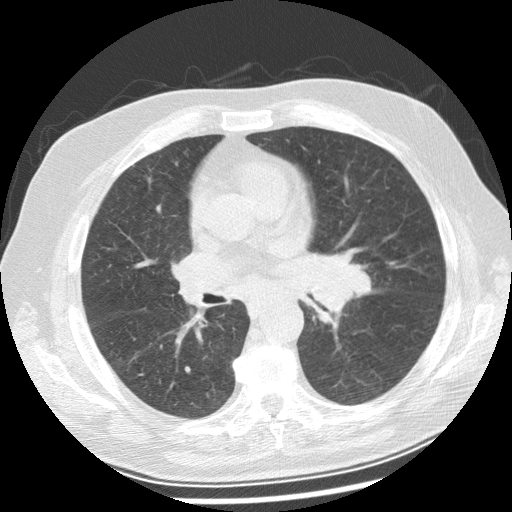
Axial slice from a low-dose chest CT screening exam; baseline screening round; lung window (W 1500 / L -600 HU); standard (soft-tissue) reconstruction kernel (STANDARD); 120 kVp; 512 × 512 image matrix. Male participant, aged 70 years at enrolment.
- Expert-annotated lung lesion, bounding box [x1, y1, x2, y2] px = [287, 241, 370, 317].
- Screening reader's record for this exam: no non-calcified nodule ≥4 mm recorded.
- Participant outcome: lung cancer diagnosed 29 days after this screen — squamous cell carcinoma, keratinizing, NOS, left main stem bronchus, moderately differentiated (G2), stage IIIB (AJCC 6th edition), 40 mm at pathology.